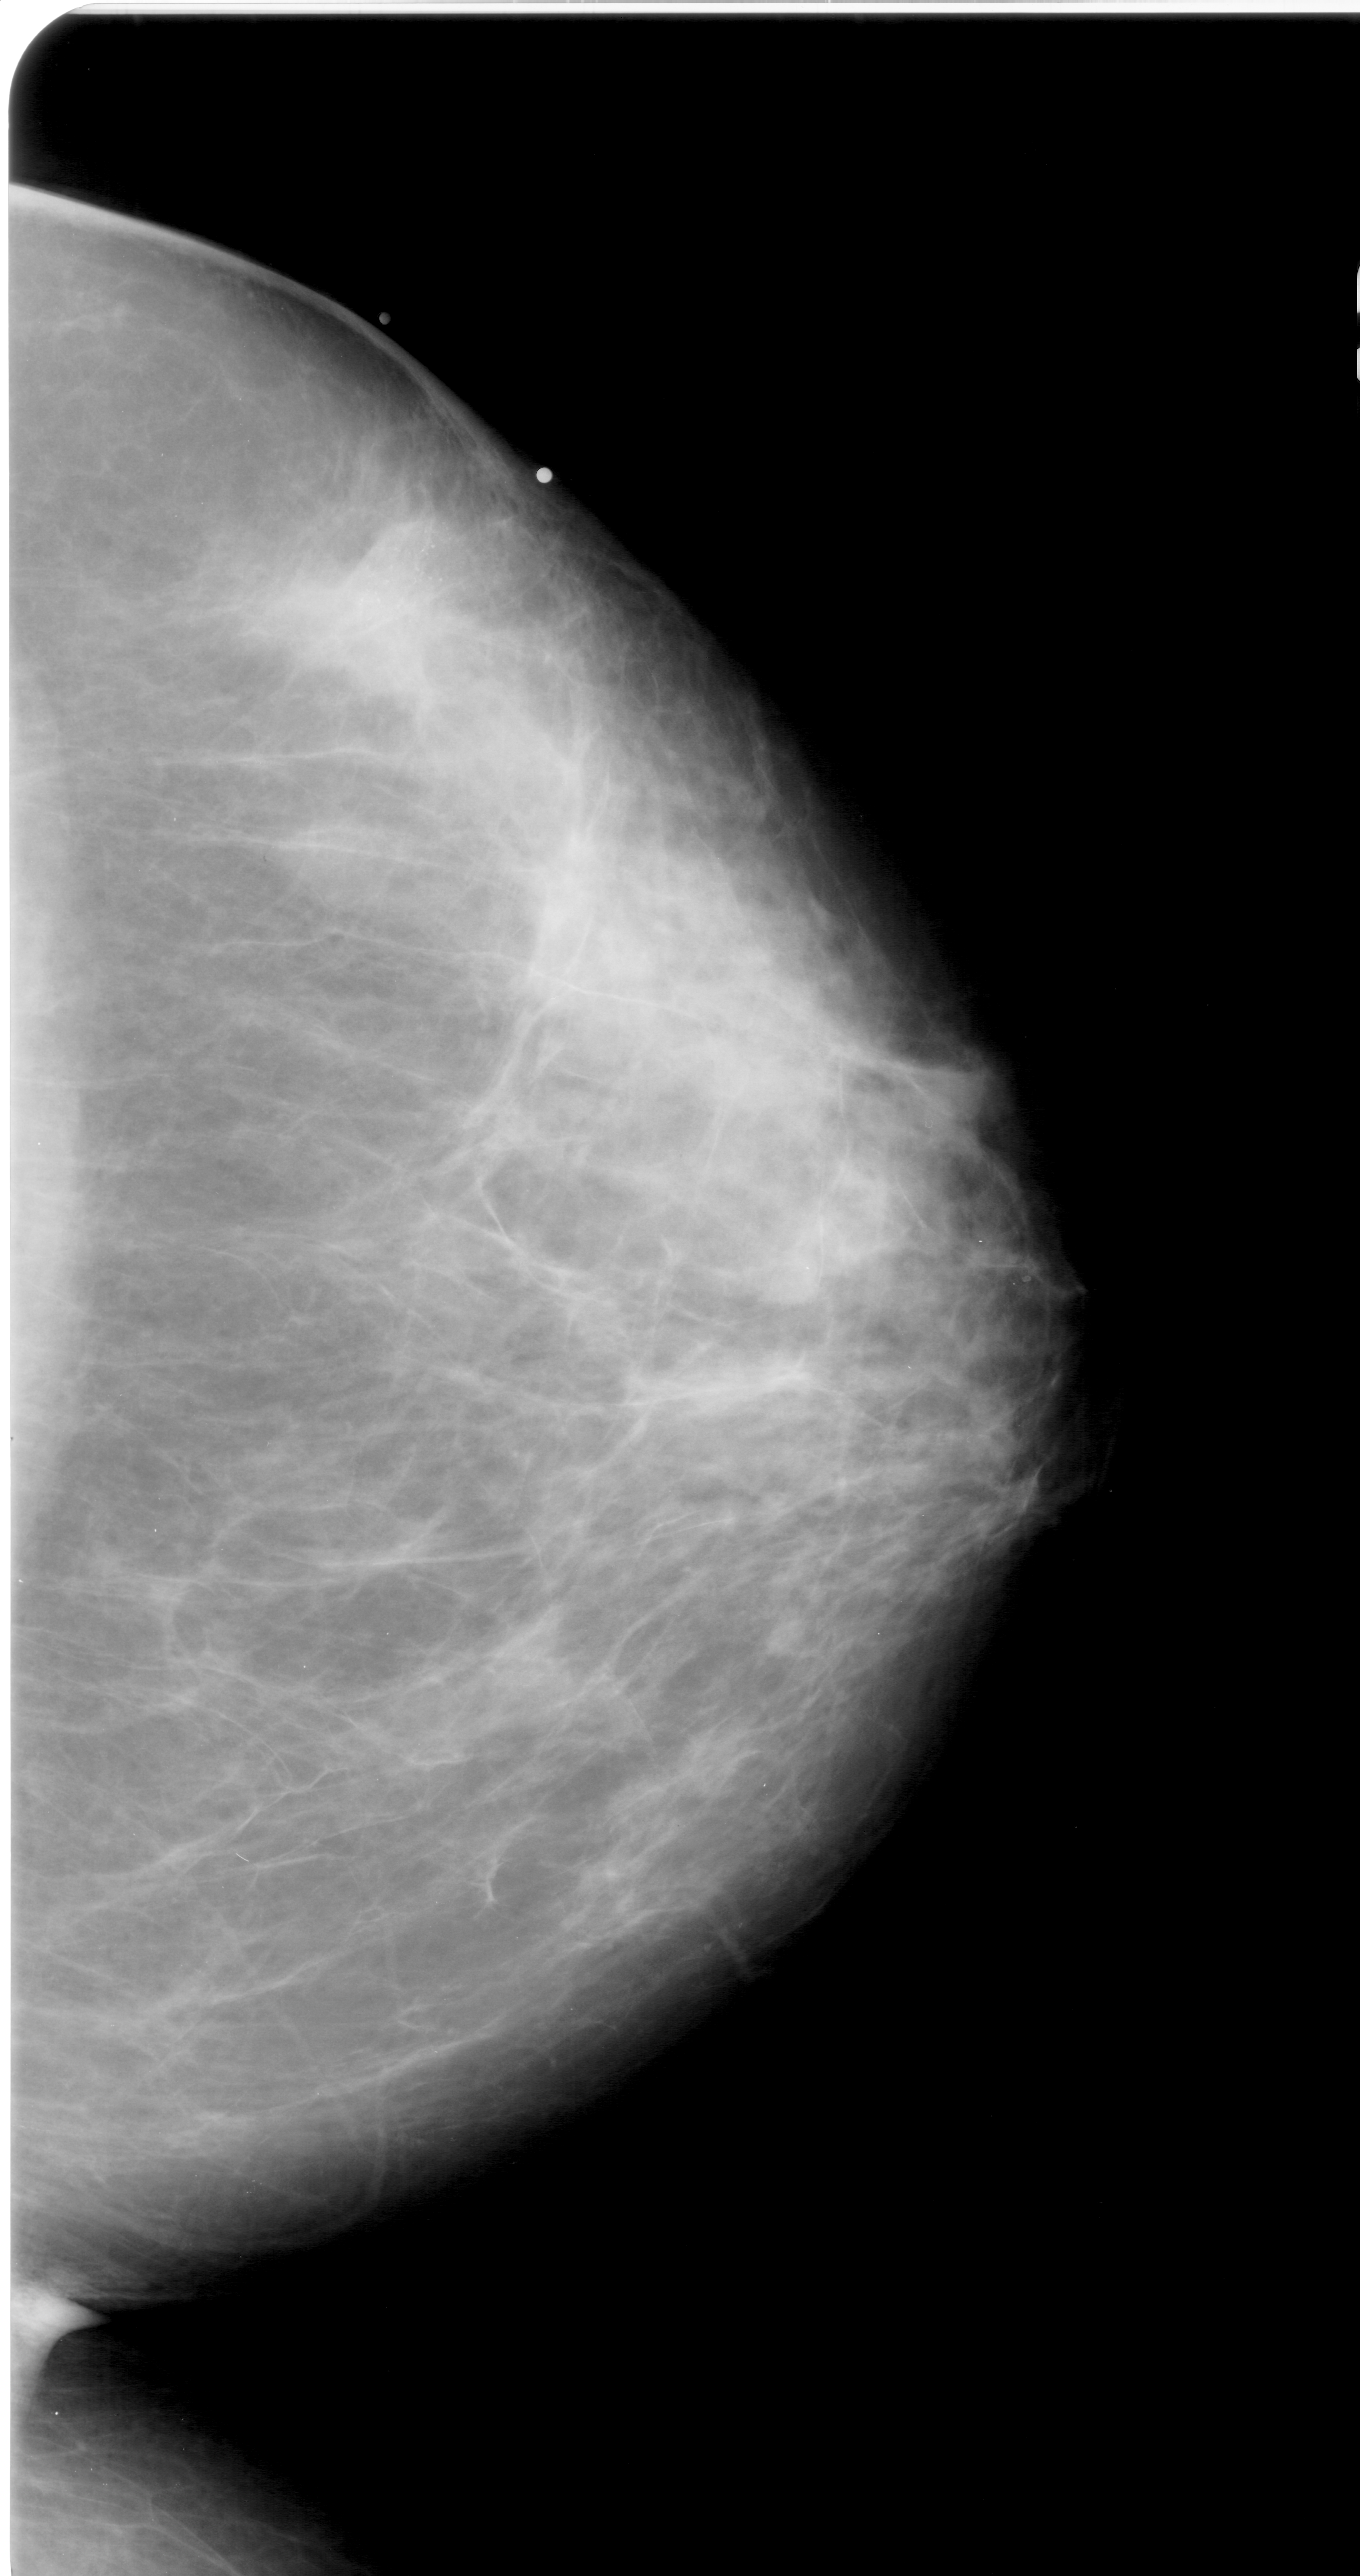
Scanned film-screen mammogram, right breast, CC view.
Marked findings (only marked abnormalities are described; nothing is implied about the rest of the image): calcifications, morphology pleomorphic, distribution clustered; BI-RADS assessment category 4; subtlety rating 4 on a 1 (subtle) to 5 (obvious) scale; pathology (as recorded): malignant.